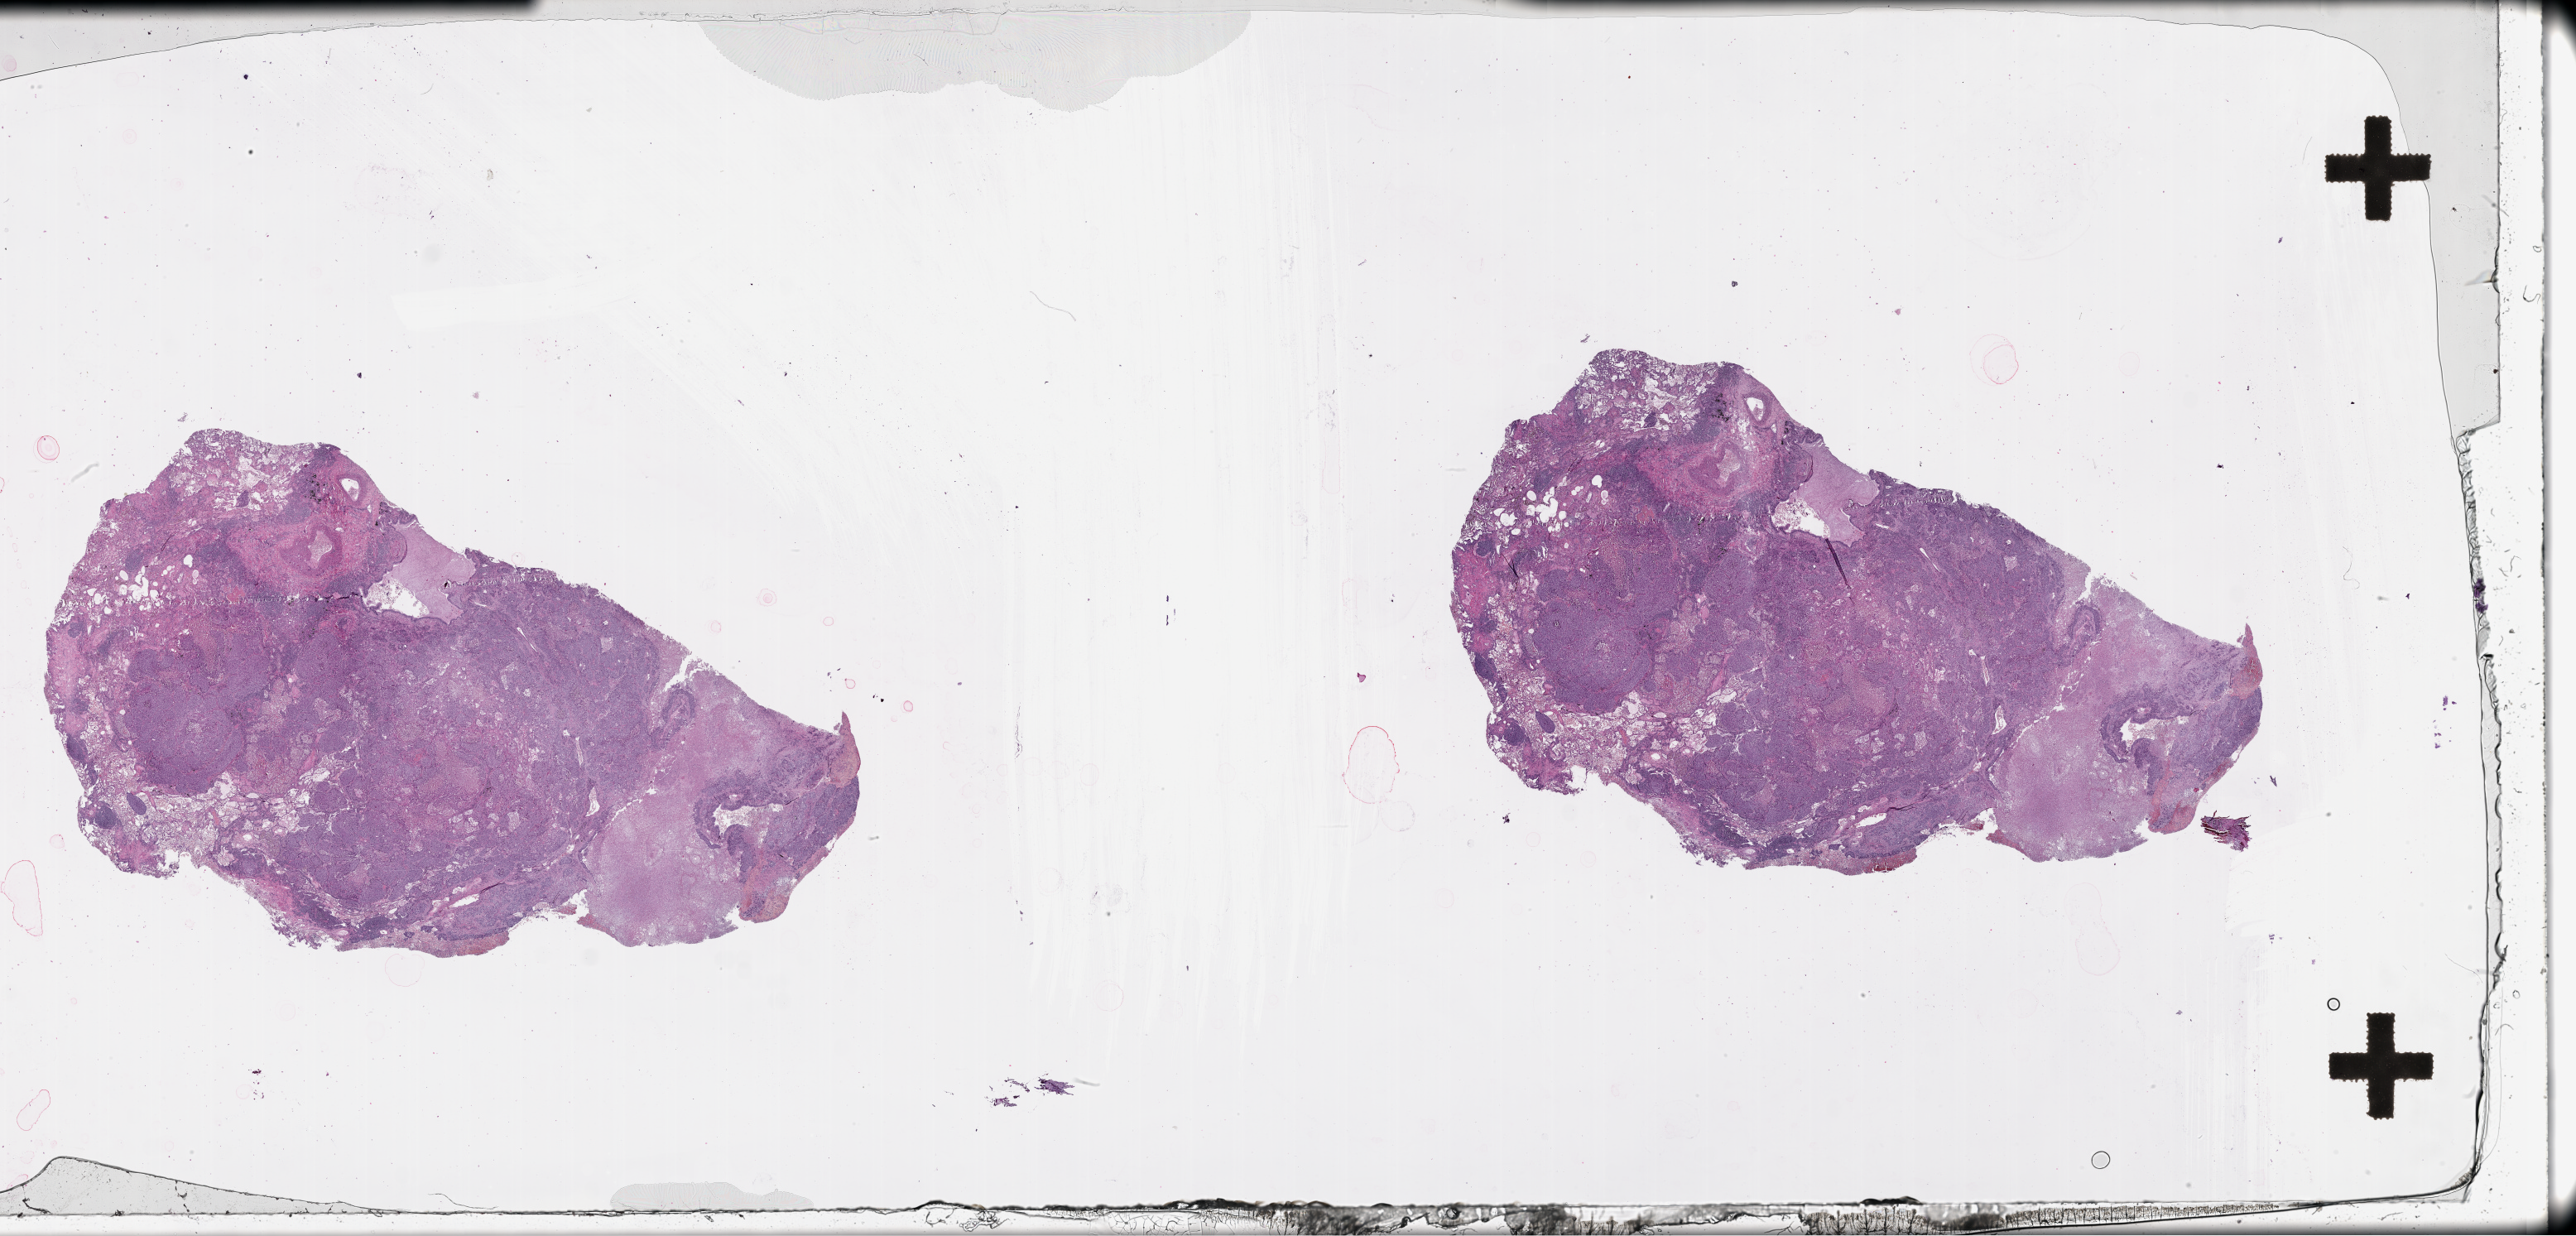
Digitized H&E-stained tissue section (whole slide) — low-resolution overview of the scanned area, about 50.1 x 24.0 mm (acquisition: 20x scan). Tumour tissue sample, lung. Patient: female, age 58 years.
Patient diagnosis (cohort enrolment): squamous cell carcinoma (lung).